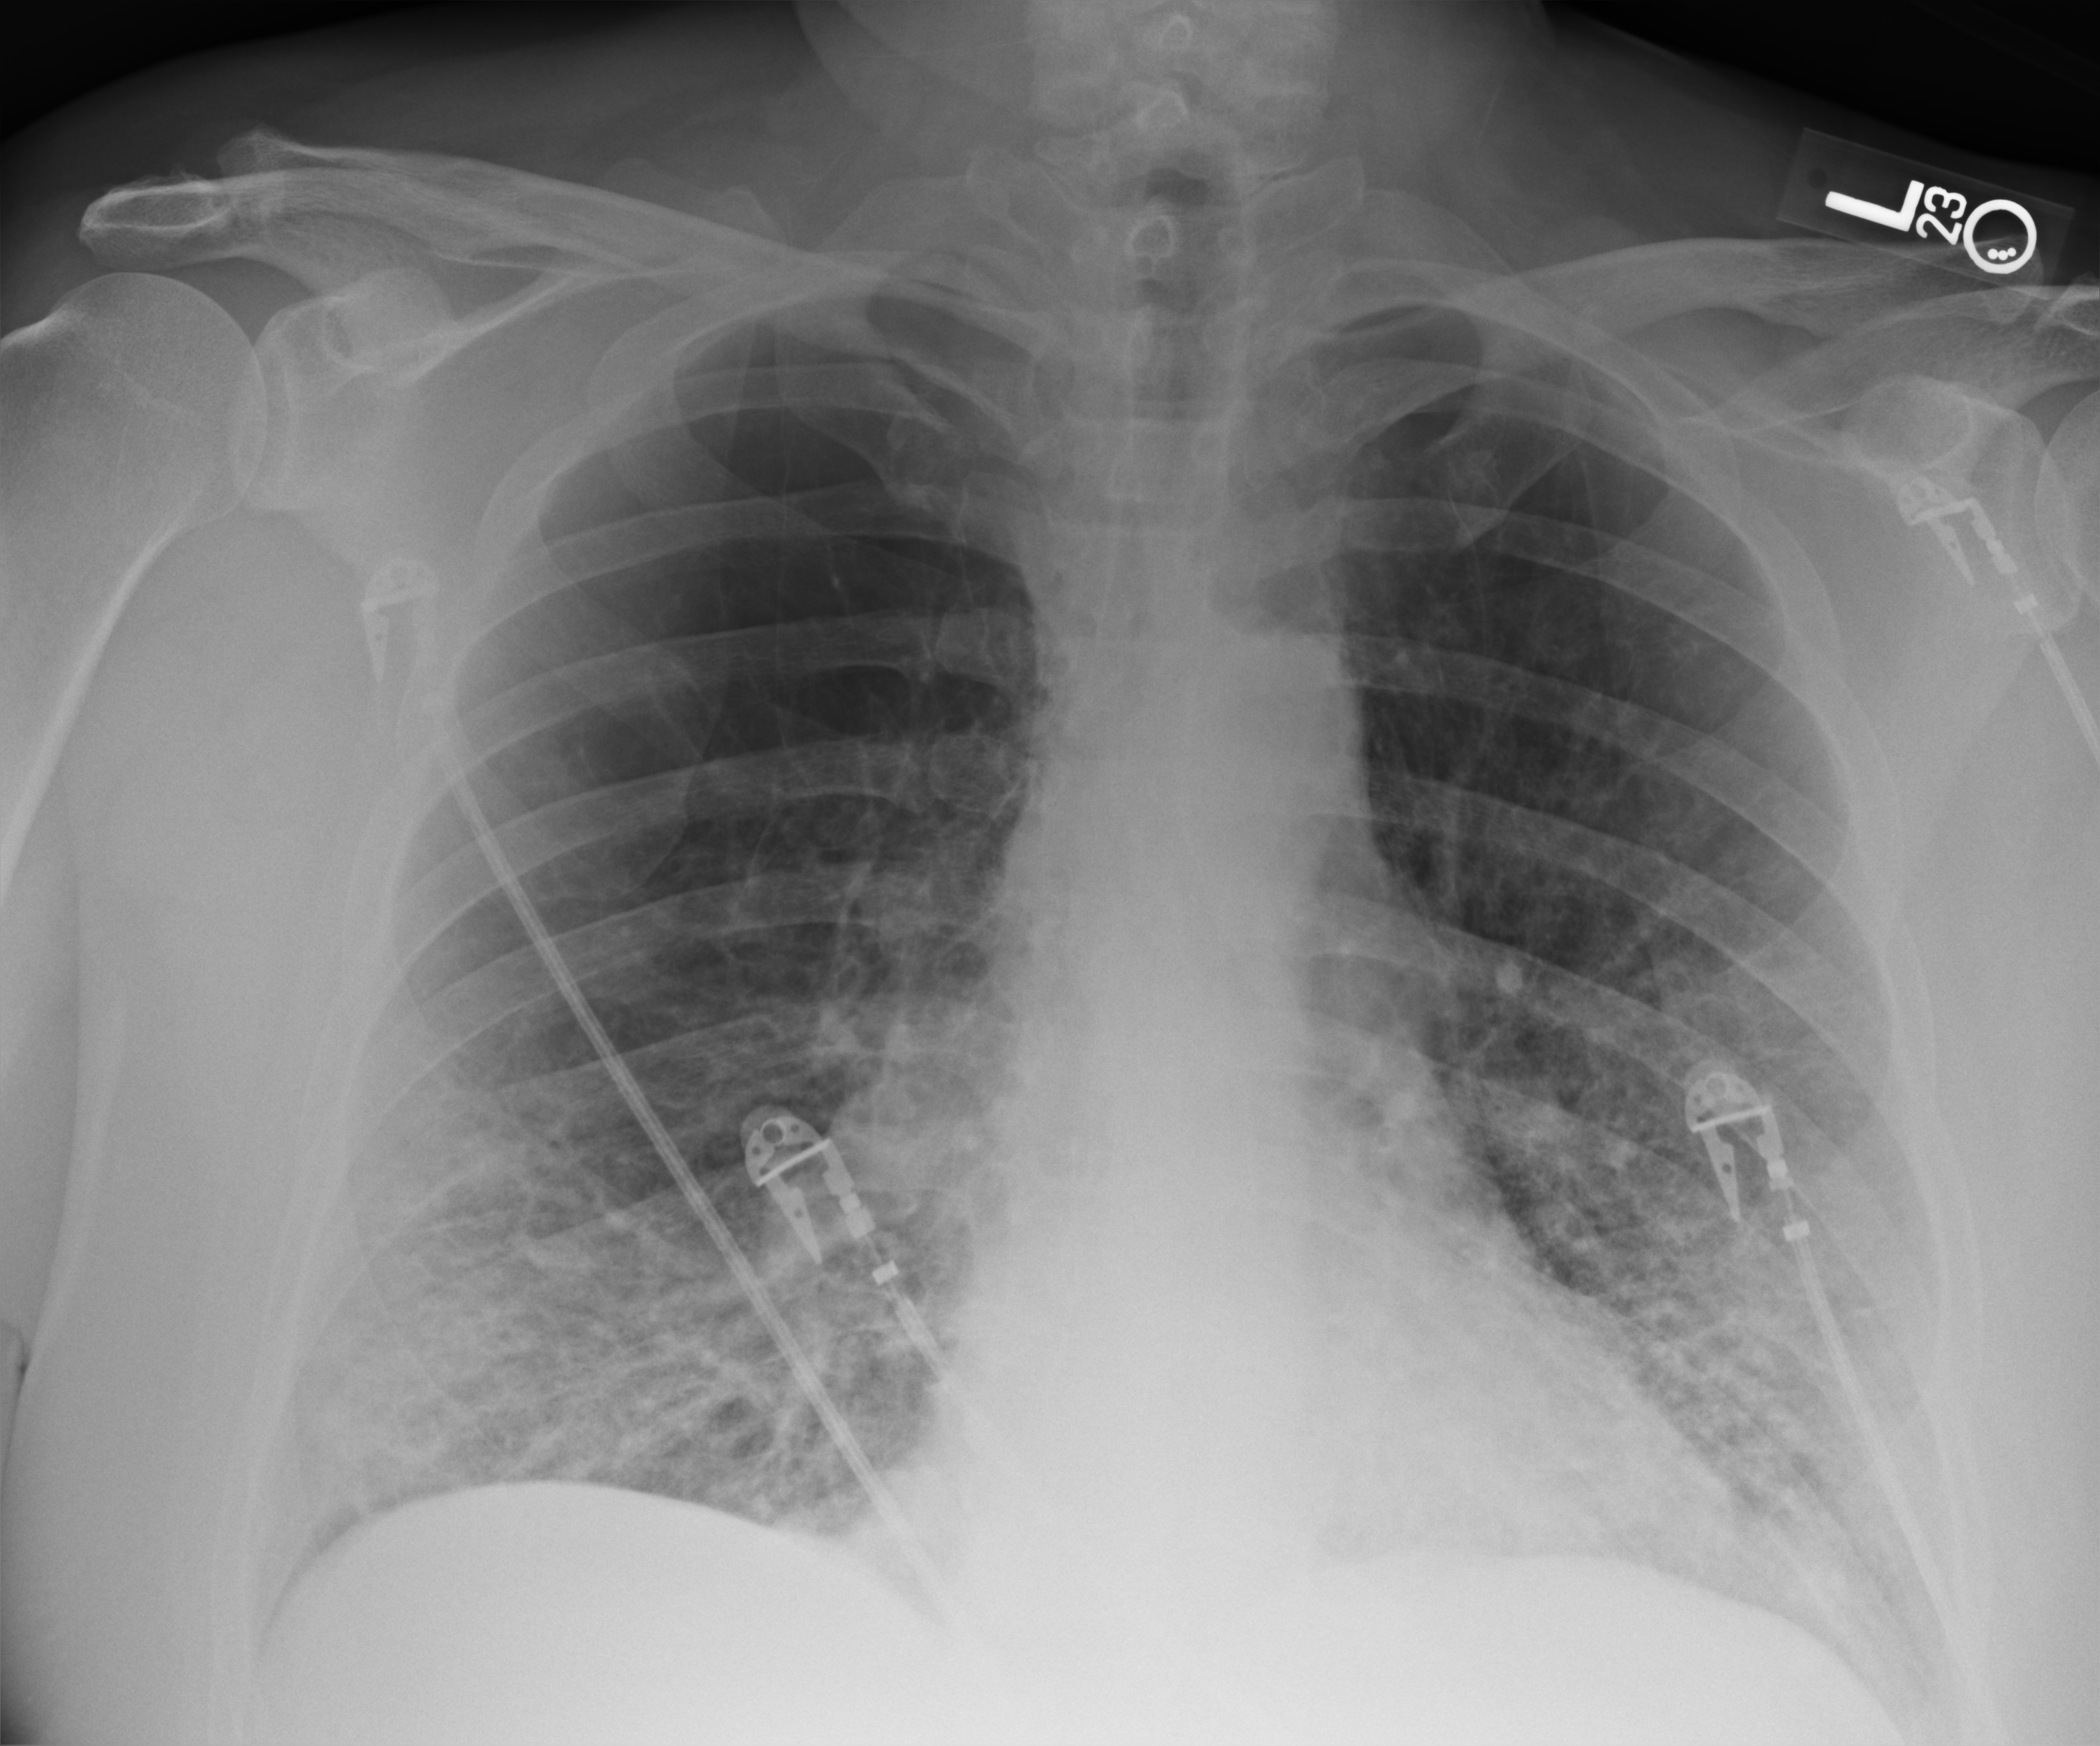
Bedside chest radiograph (computed radiography). Adult patient hospitalised with COVID-19, age 18–59 years.
Hospital-stay facts (about this admission, not read from this image; timing relative to this image not recorded): mechanically ventilated during this hospital stay: yes; length of hospital stay: 9 days.